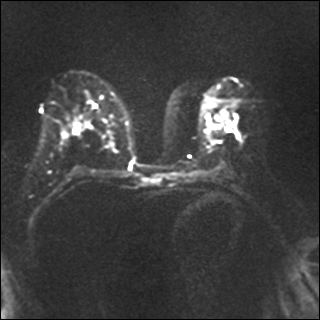
Breast MRI, one axial slice; slice 20 of 35 in the series (ordered by position); diffusion-weighted series; image 2 of 4 stored at this slice position (different b-values; order by instance number); 1.5 T; 4 mm slice thickness; 320 × 320 image matrix, field of view 320 × 320 mm. Female patient.
Structures marked on this image (expert manual segmentation):
- tumour on diffusion-weighted imaging: bounding box [x1, y1, x2, y2] px = [228, 123, 232, 128]